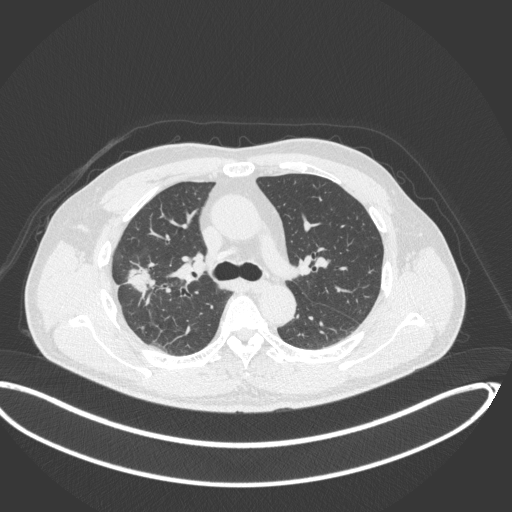
Chest CT, one axial slice. Position 224 of 341 along the scan axis. Lung window (W 1500 / L -600 HU). 512 × 512 image matrix, field of view 439 × 439 mm. Patient: male, 63 years. Case-level facts recorded for this patient, not image findings: clinical TNM (as recorded): T1c N0 M0.
Annotated regions visible in this slice (rectangle marked by the reading radiologist):
- lung tumour (recorded histology: adenocarcinoma): bounding box (x1, y1, x2, y2) in pixels: (125, 254, 162, 306)